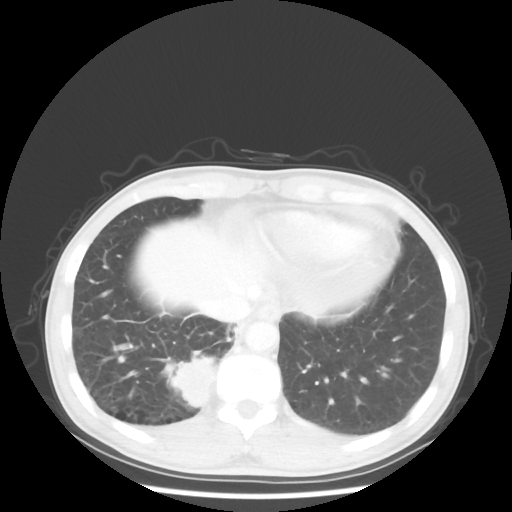
Chest CT, one axial slice; position 11 of 58 along the scan axis; reconstruction kernel STANDARD; 100 kVp; lung window (W 1500 / L -600 HU); 512 × 512 image matrix, field of view 360 × 360 mm. Male patient, age 56 years. From the clinical record (not read from this slice): clinical TNM (as recorded): T2 N1 M1; histopathological grade: G1.
Annotated regions visible in this slice (bounding box drawn by a radiologist):
- lung tumour (recorded histology: adenocarcinoma): bounding box (x1, y1, x2, y2) in pixels: (167, 349, 216, 412)